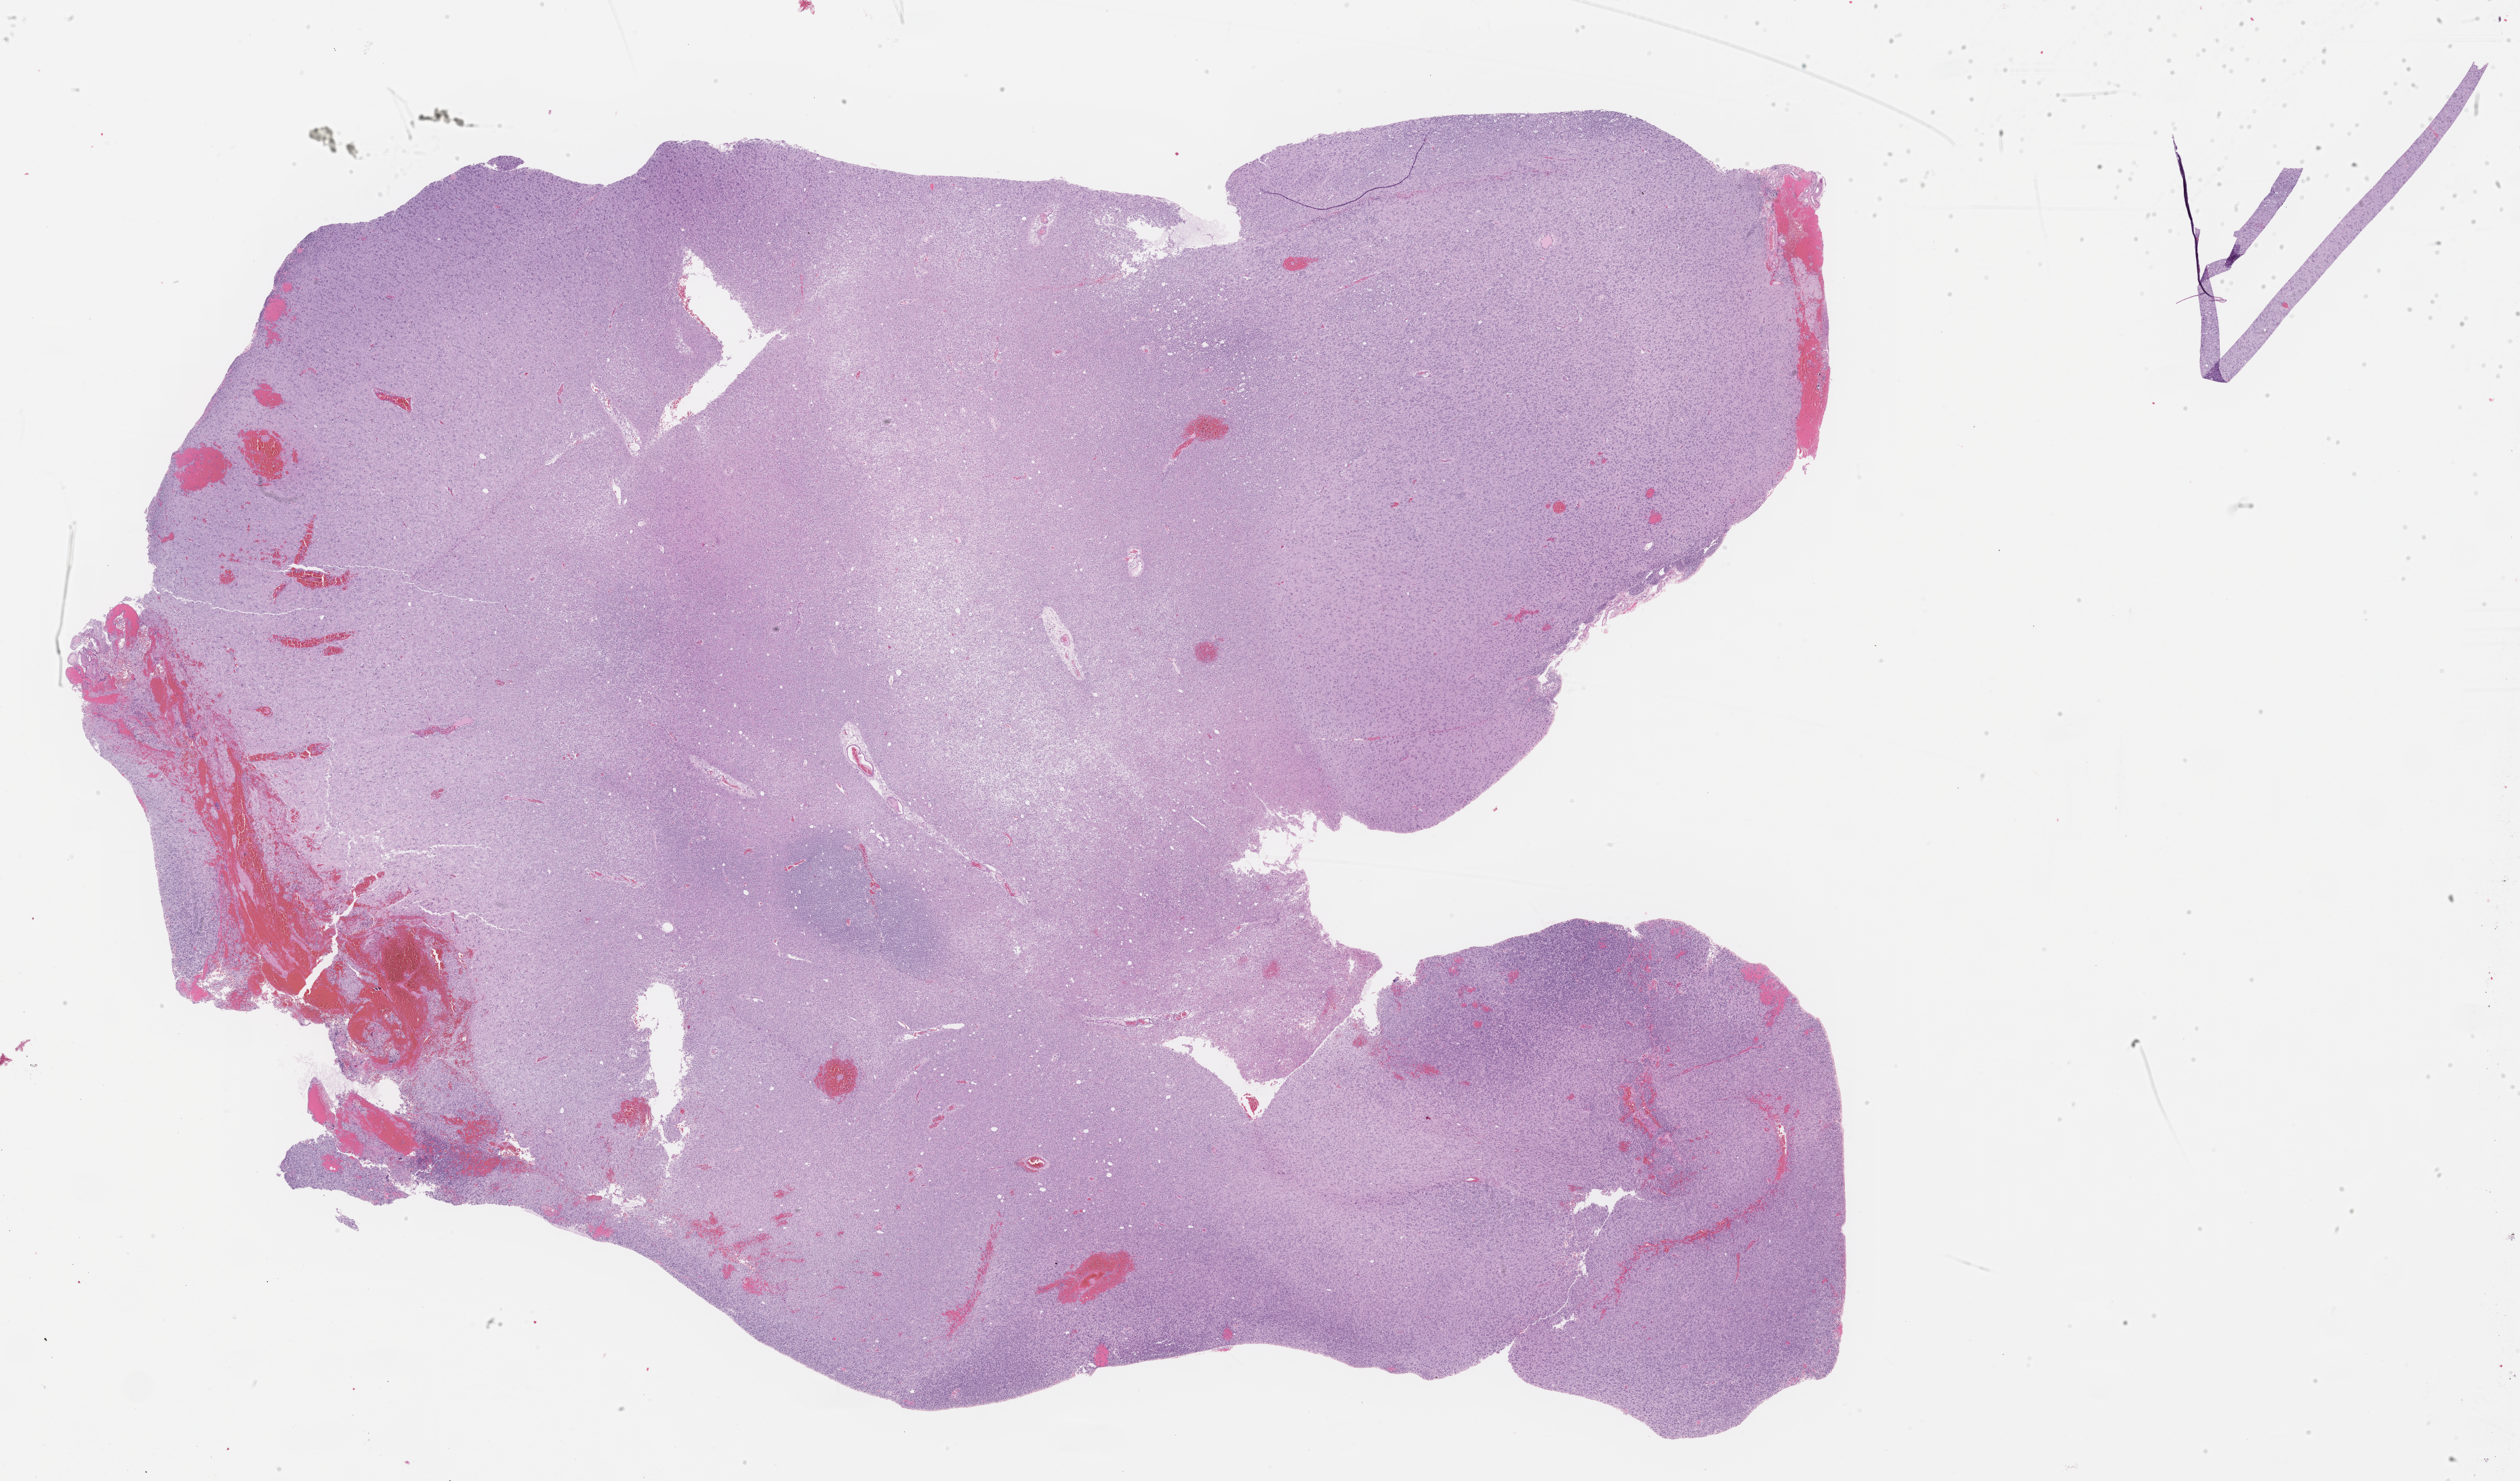
H&E whole-slide image, shown as a low-resolution overview of the whole scanned area (about 30.0 x 17.6 mm, slide scanned at 40x). Formalin-fixed paraffin-embedded (FFPE) diagnostic section. Brain, primary tumour sample. Patient: female, age at initial diagnosis 53 years. Histologic grade: G2 (moderately differentiated).
Histologic diagnosis: Oligodendroglioma, NOS.